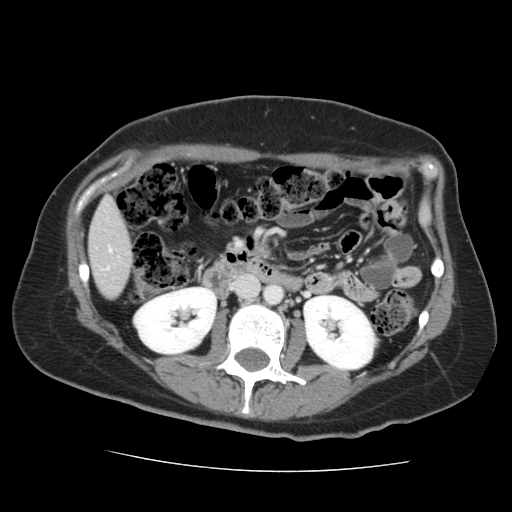
Contrast-enhanced abdominal CT, one axial slice; position 51 of 144 along the scan axis; soft-tissue window (W 400 / L 40 HU); 2.5 mm slice thickness; 512 × 512 image matrix. Female patient, age 46 years. From the clinical record (not read from this slice): diagnosis: colorectal cancer liver metastases, imaged before liver resection; multiple liver metastases: no; largest metastasis: 2.8 cm; disease in both lobes: no.
Outlined on this slice (expert manual segmentation):
- liver: box from (x=90, y=201) to (x=131, y=298) px
- planned liver remnant (the part of the liver to remain after resection): (x=90, y=201)–(x=131, y=294)
- portal vein (with intrahepatic branches): (x=109, y=250)–(x=111, y=252)